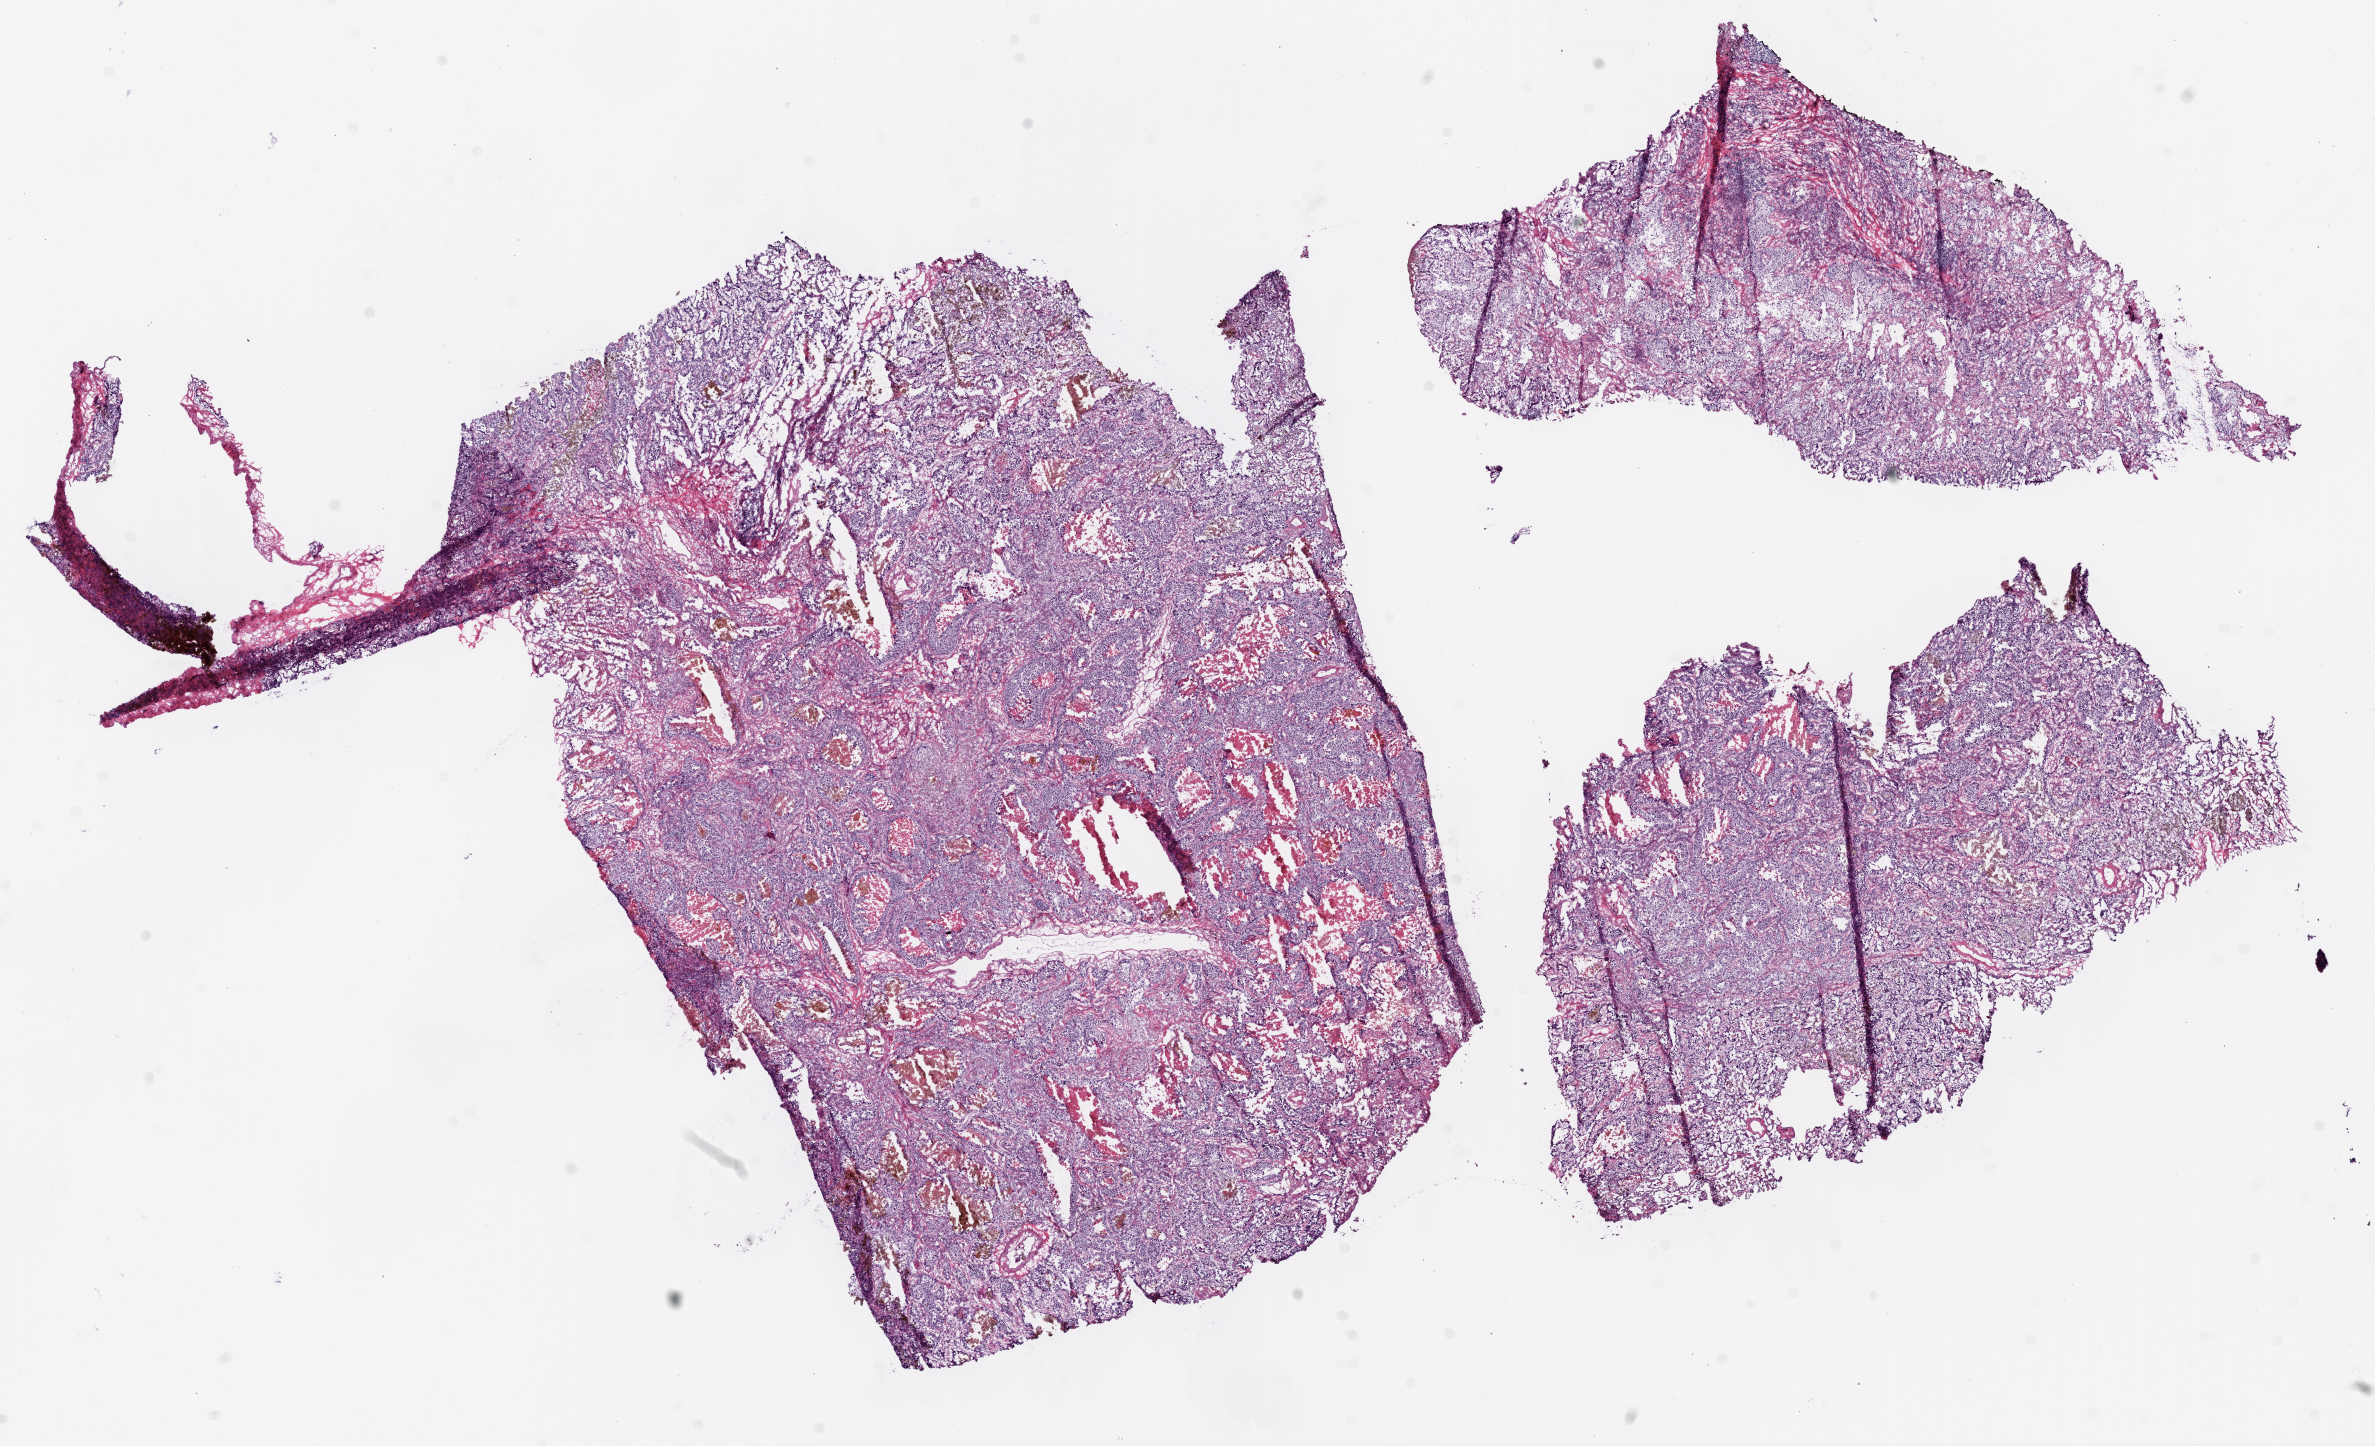
H&E-stained whole-slide image — whole scanned area (about 19.1 x 11.6 mm, slide scanned at 20x) shown as a low-resolution overview; frozen section from the top of the tissue portion; lung, primary tumour sample. Patient: male, age at initial diagnosis 65 years. Composition of this section per pathologist review: tumour cells 75%, tumour nuclei 80%, normal cells 0%, stromal cells 10%, necrosis 15%.
• AJCC pathologic stage: IA
• diagnosis: Adenocarcinoma, NOS (upper lobe, lung)